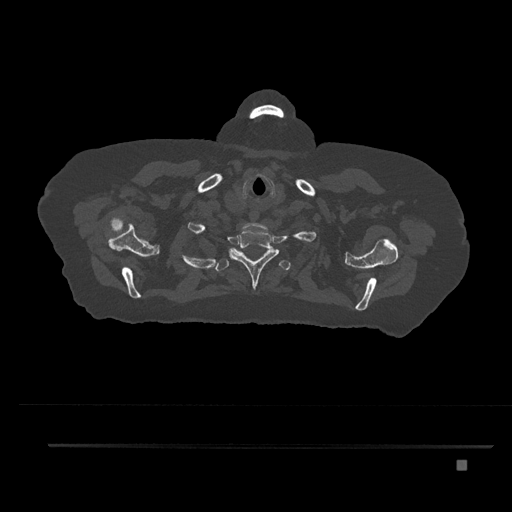
CT including the spine, one axial slice. 120 kVp. Bone window (W 1800 / L 400 HU). 0.5 mm slice thickness. 512 × 512 image matrix, field of view 437 × 437 mm. Patient: female, 76 years. From the clinical record (not read from this slice): primary cancer: lung.
Annotated regions visible in this slice (semi-automatically segmented with operator editing):
- T1 vertebra: box from (x=229, y=227) to (x=280, y=290) px
- T2 vertebra: (x=207, y=248)–(x=291, y=272)